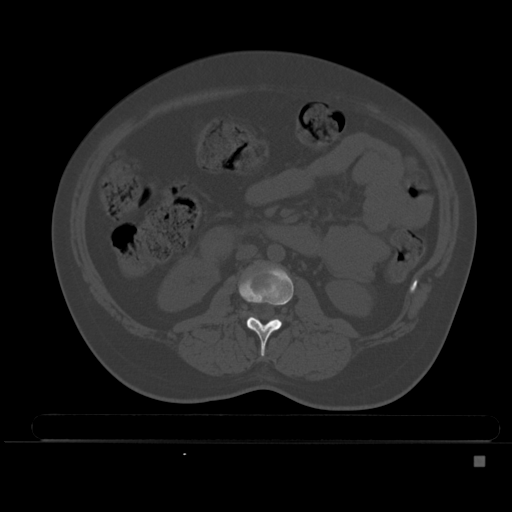
CT including the spine, one axial slice; slice 167 of 495 in the series (ordered by position); bone window (W 1800 / L 400 HU); 1.5 mm slice thickness; 512 × 512 image matrix. Female patient, age 33 years. Case-level facts recorded for this patient, not image findings: primary cancer: breast.
Outlined on this slice (semi-automatic segmentation, software-assisted and operator-edited):
- L2 vertebra: bounding box <238,265,294,356> (left, top, right, bottom; pixels)